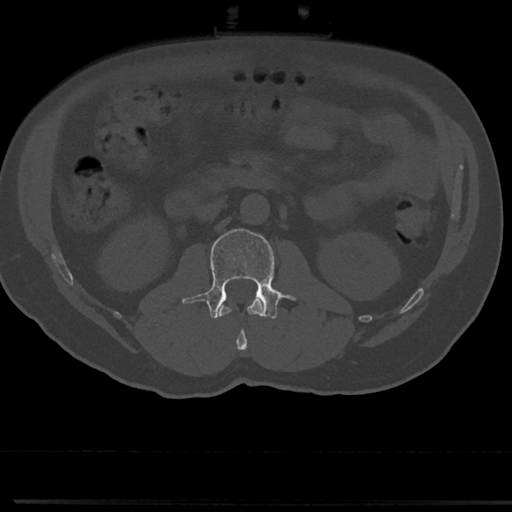
CT including the spine, one axial slice; slice 31 of 817 in the series (ordered by position); reconstruction kernel Br40s/3; bone window (W 1800 / L 400 HU); 512 × 512 image matrix, field of view 355 × 355 mm. Male patient, age 61 years. From the clinical record (not read from this slice): primary cancer: prostate.
Outlined on this slice (semi-automatic segmentation, software-assisted and operator-edited):
- L1 vertebra: bounding box [x1, y1, x2, y2] px = [219, 298, 263, 352]
- L2 vertebra: [191, 228, 293, 319]